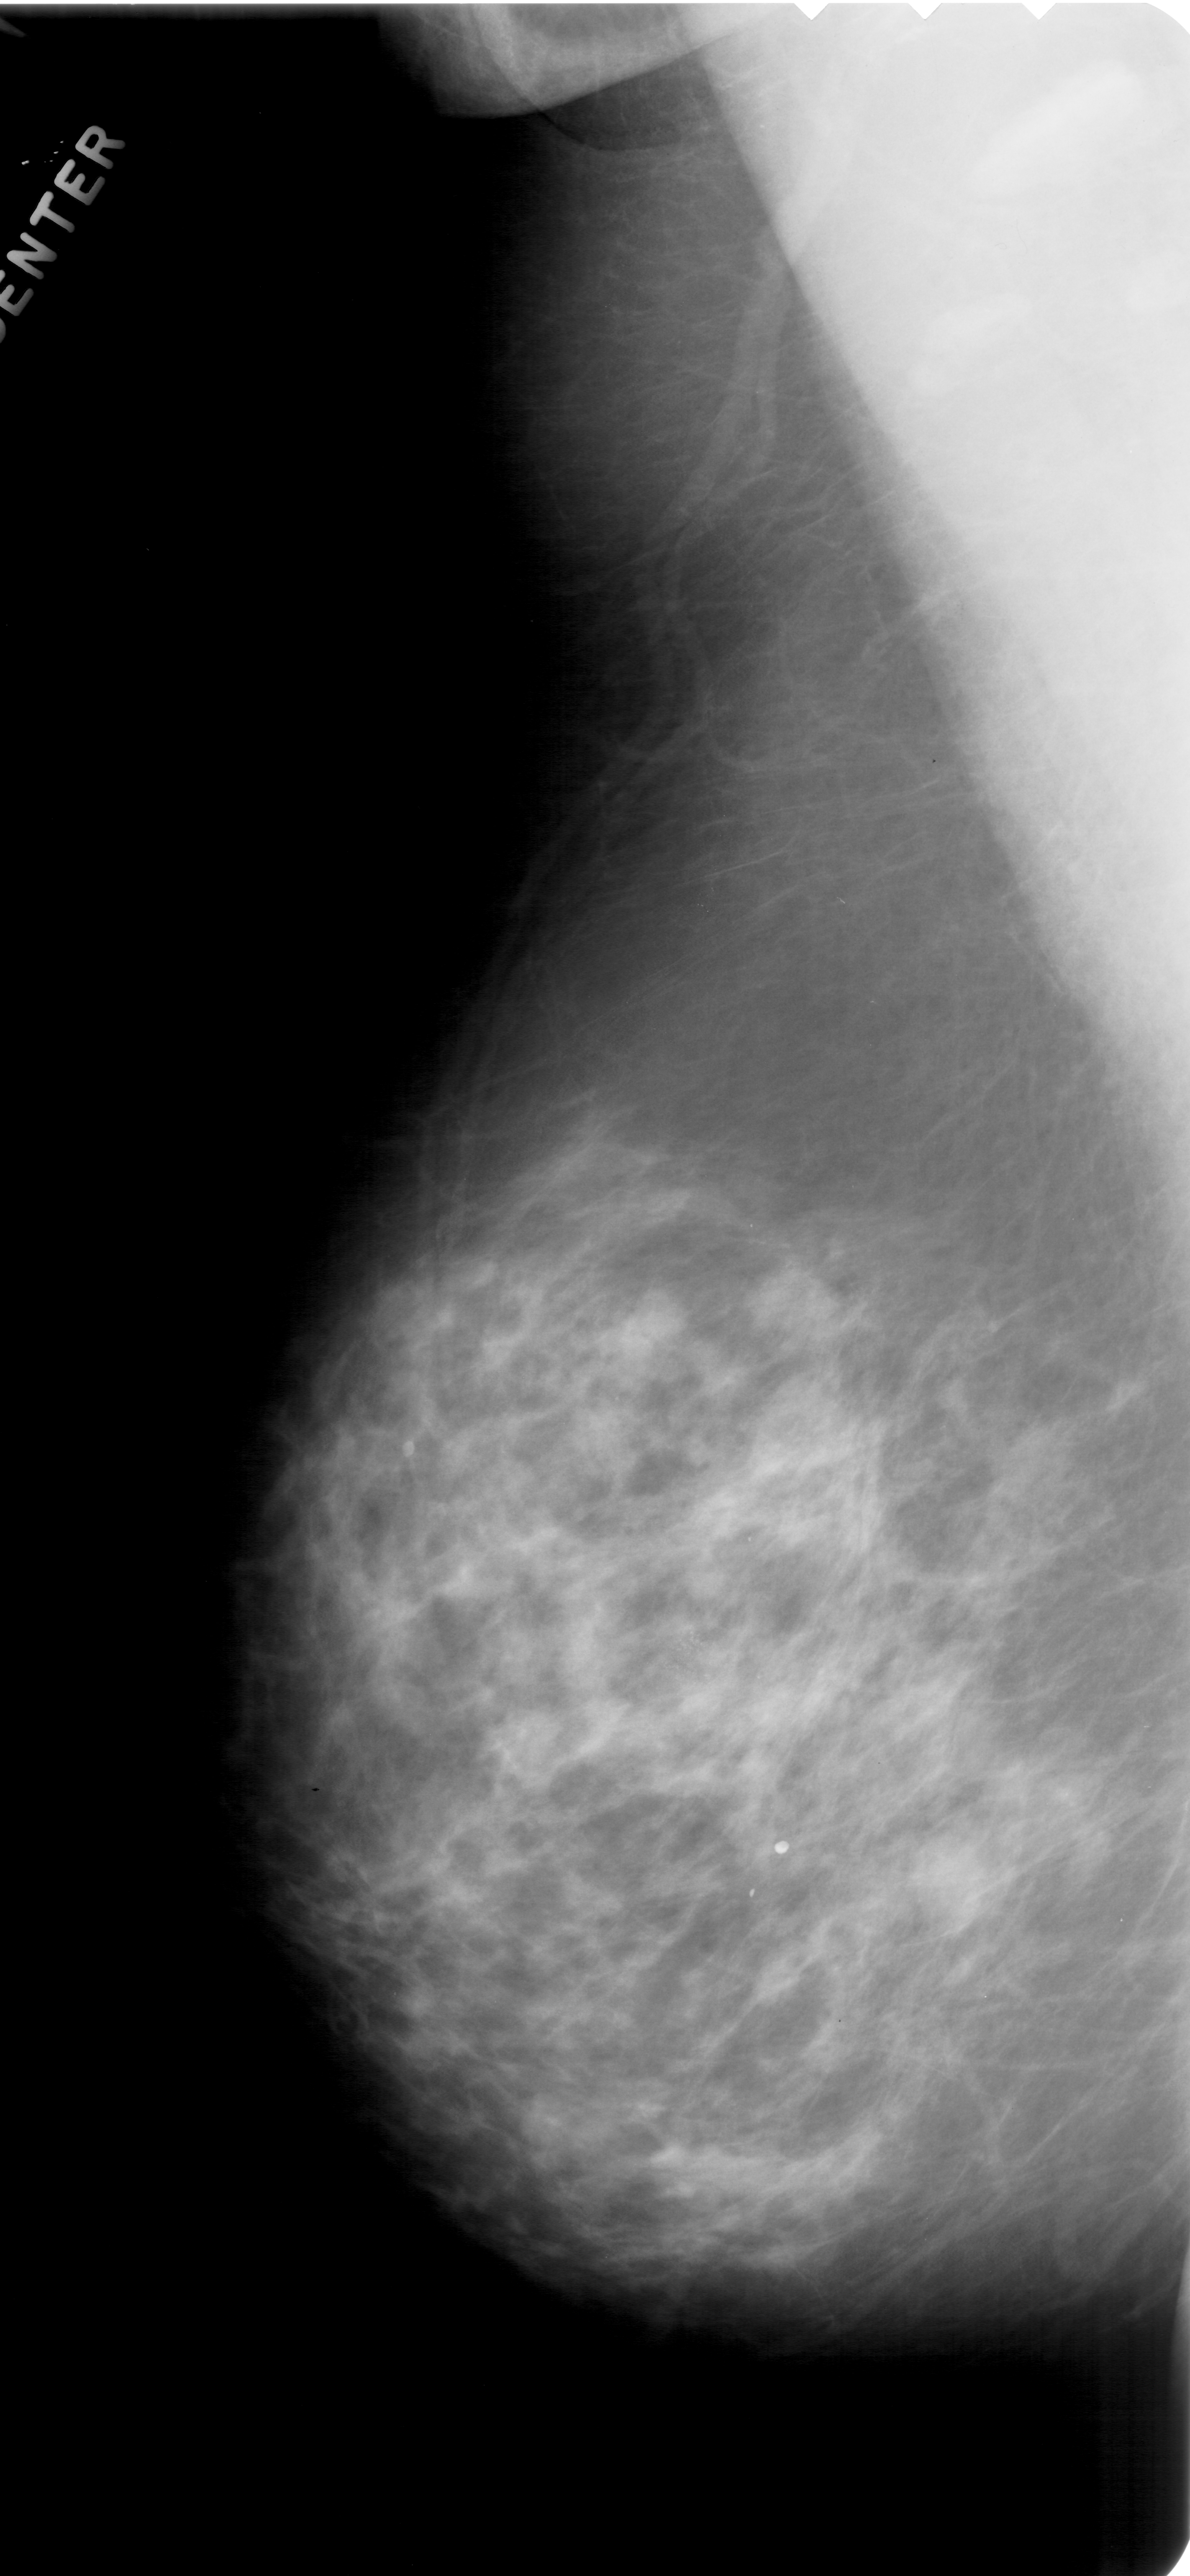
Scanned film-screen mammogram; left breast; MLO view; BI-RADS breast density category 3 (scale 1–4).
- Finding: calcifications, morphology pleomorphic, distribution clustered; BI-RADS assessment category 4; pathology (as recorded): malignant.